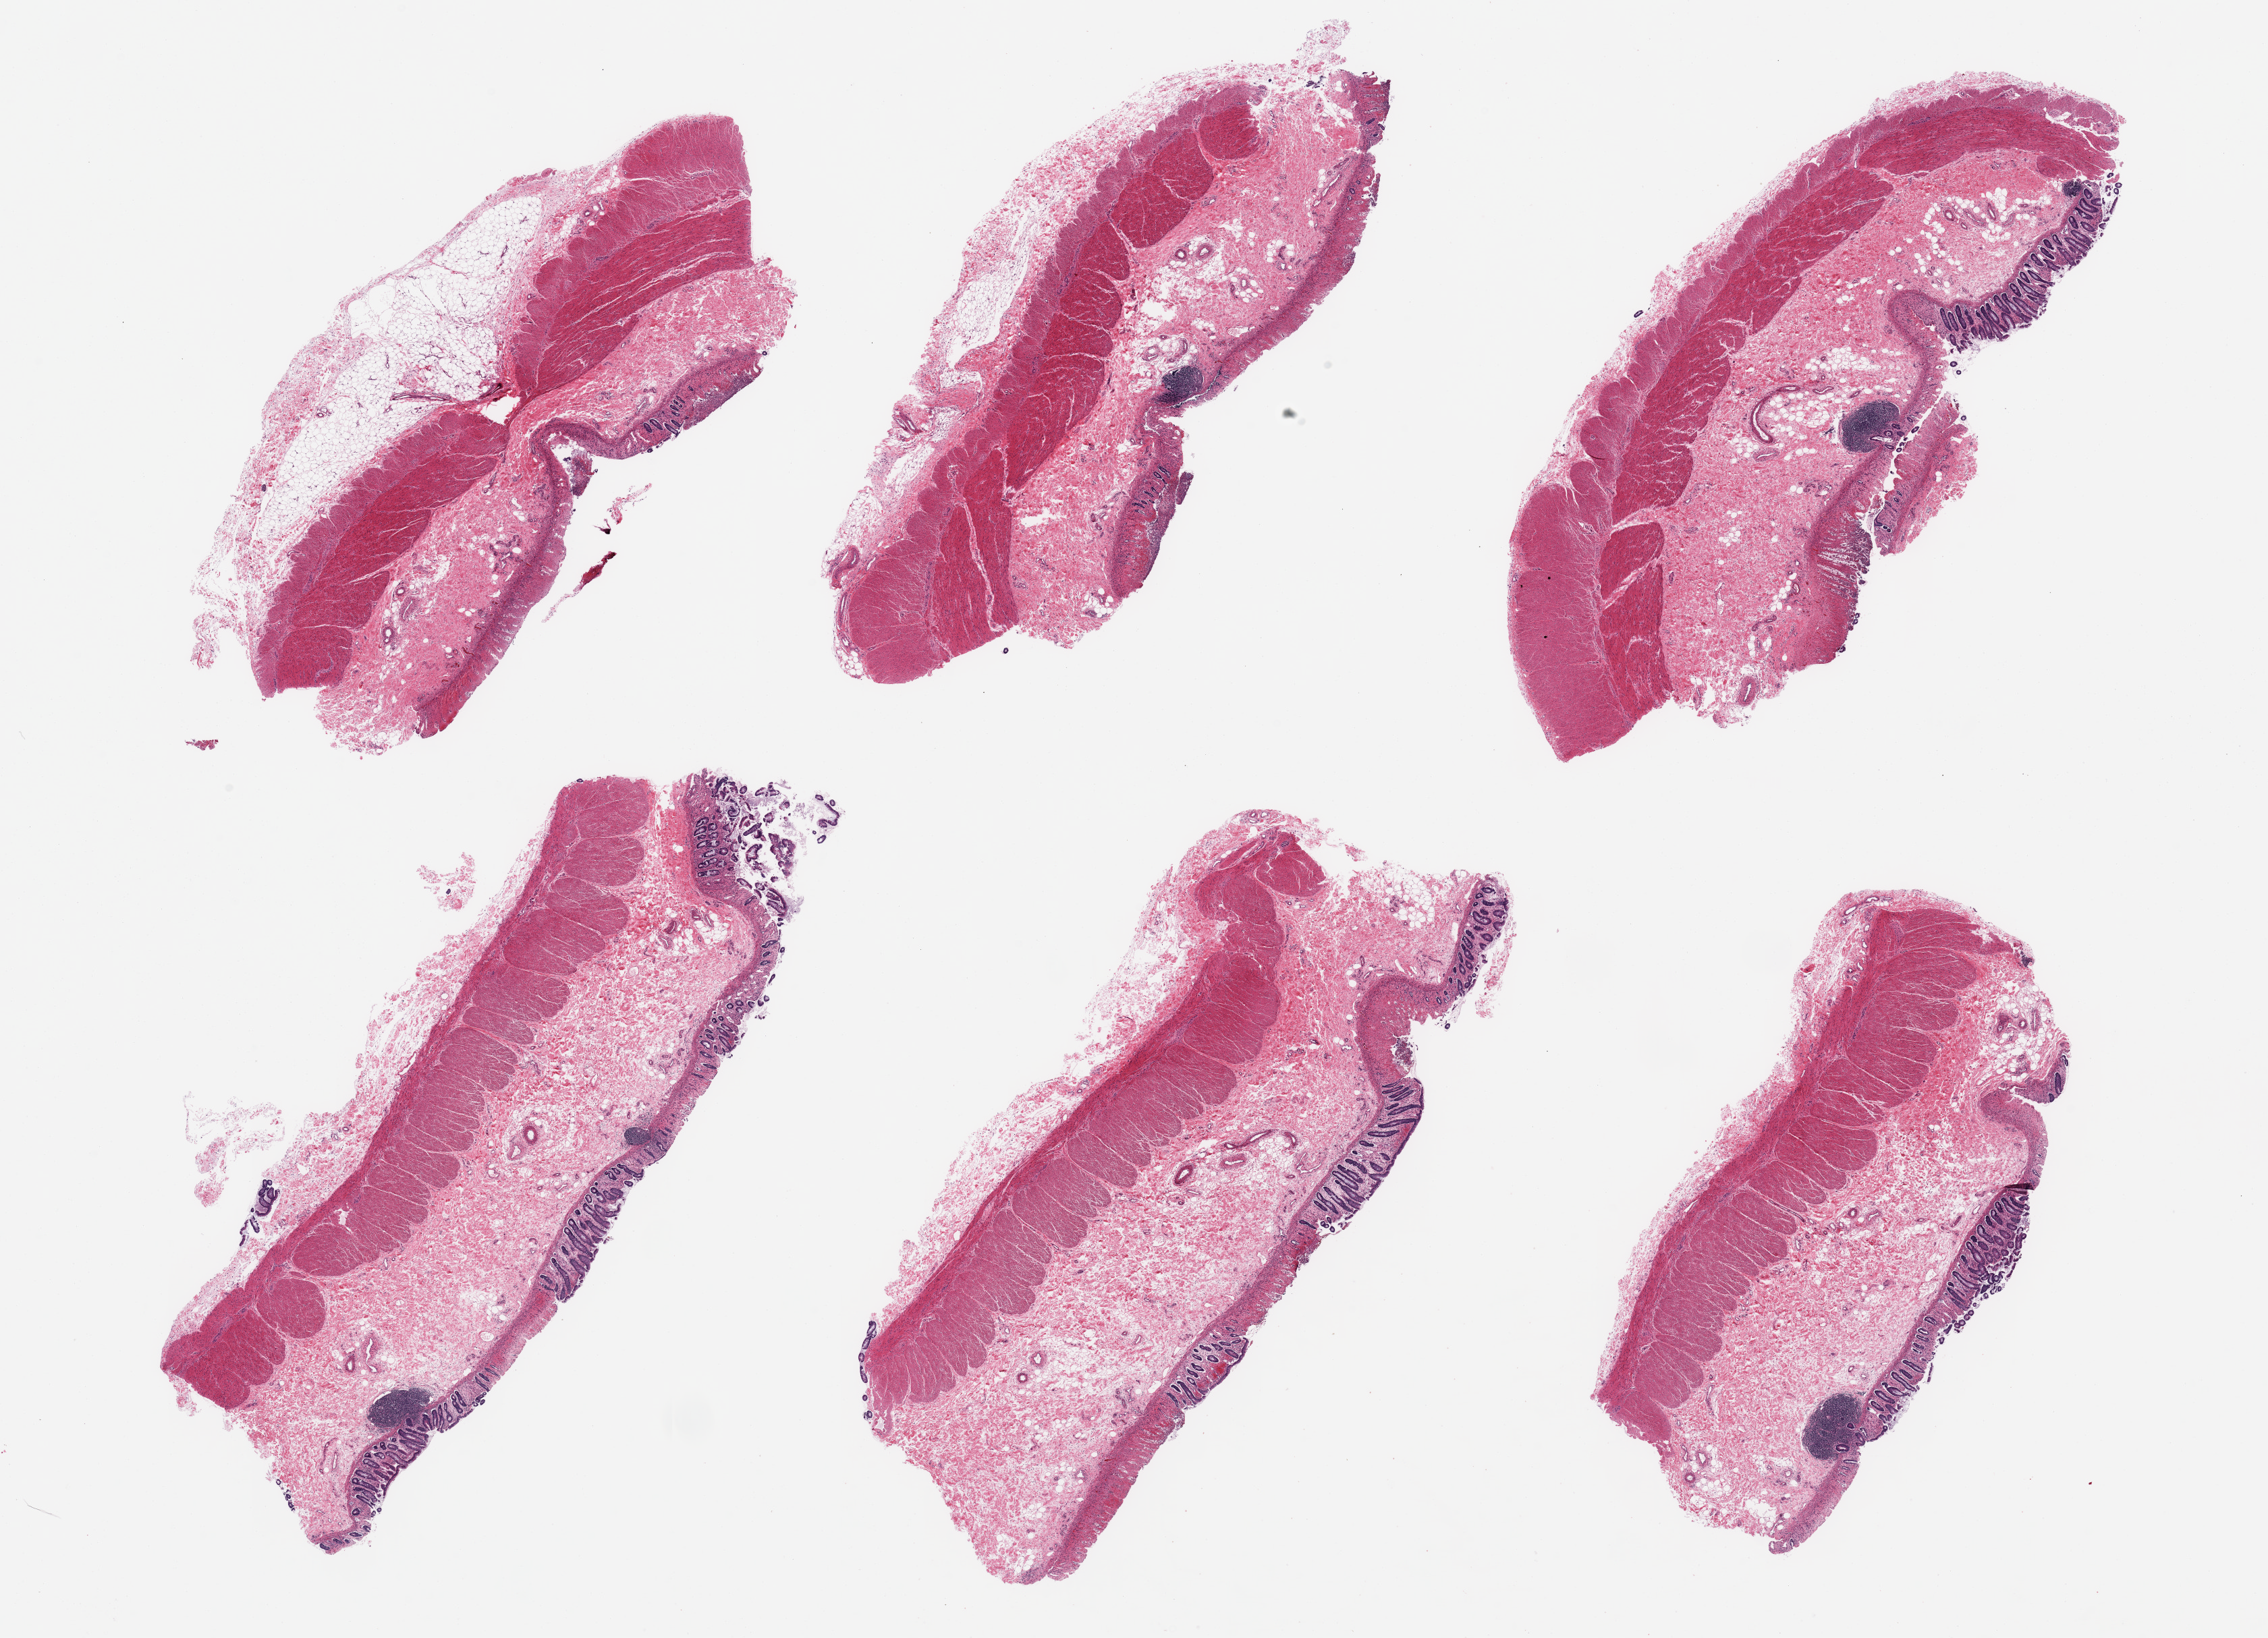
Digitized hematoxylin and eosin (H&E)-stained section, a low-resolution overview of the entire scanned area, about 26.6 x 19.2 mm; PAXgene-fixed, paraffin-embedded tissue; section of transverse colon (target tissue); tissue donor sample. Donor: female.
• review note (as recorded): 6 pieces; moderate to severe autolysis of colonic mucosa; muscularis preserved; up to 1.6mm attached serosa